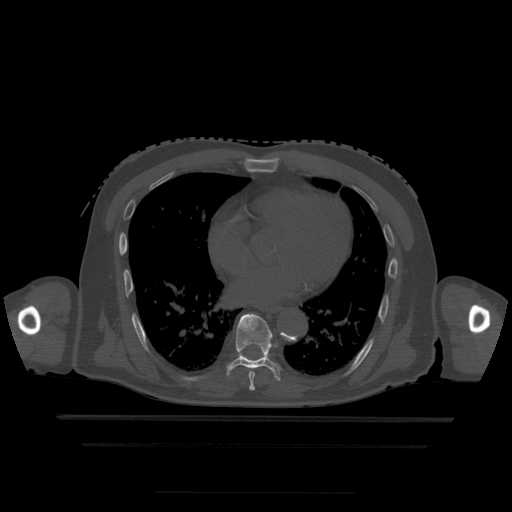
CT including the spine, one axial slice. Slice 282 of 522 in the series (ordered by position). Bone window (W 1800 / L 400 HU). 1.25 mm slice thickness. 512 × 512 image matrix. Patient age 68 years. Case-level facts recorded for this patient, not image findings: primary cancer: urothelial.
Structures marked on this image (semi-automatic segmentation, software-assisted and operator-edited):
- T7 vertebra: bounding box <249,372,255,393> (left, top, right, bottom; pixels)
- T8 vertebra: <227,314,281,381>